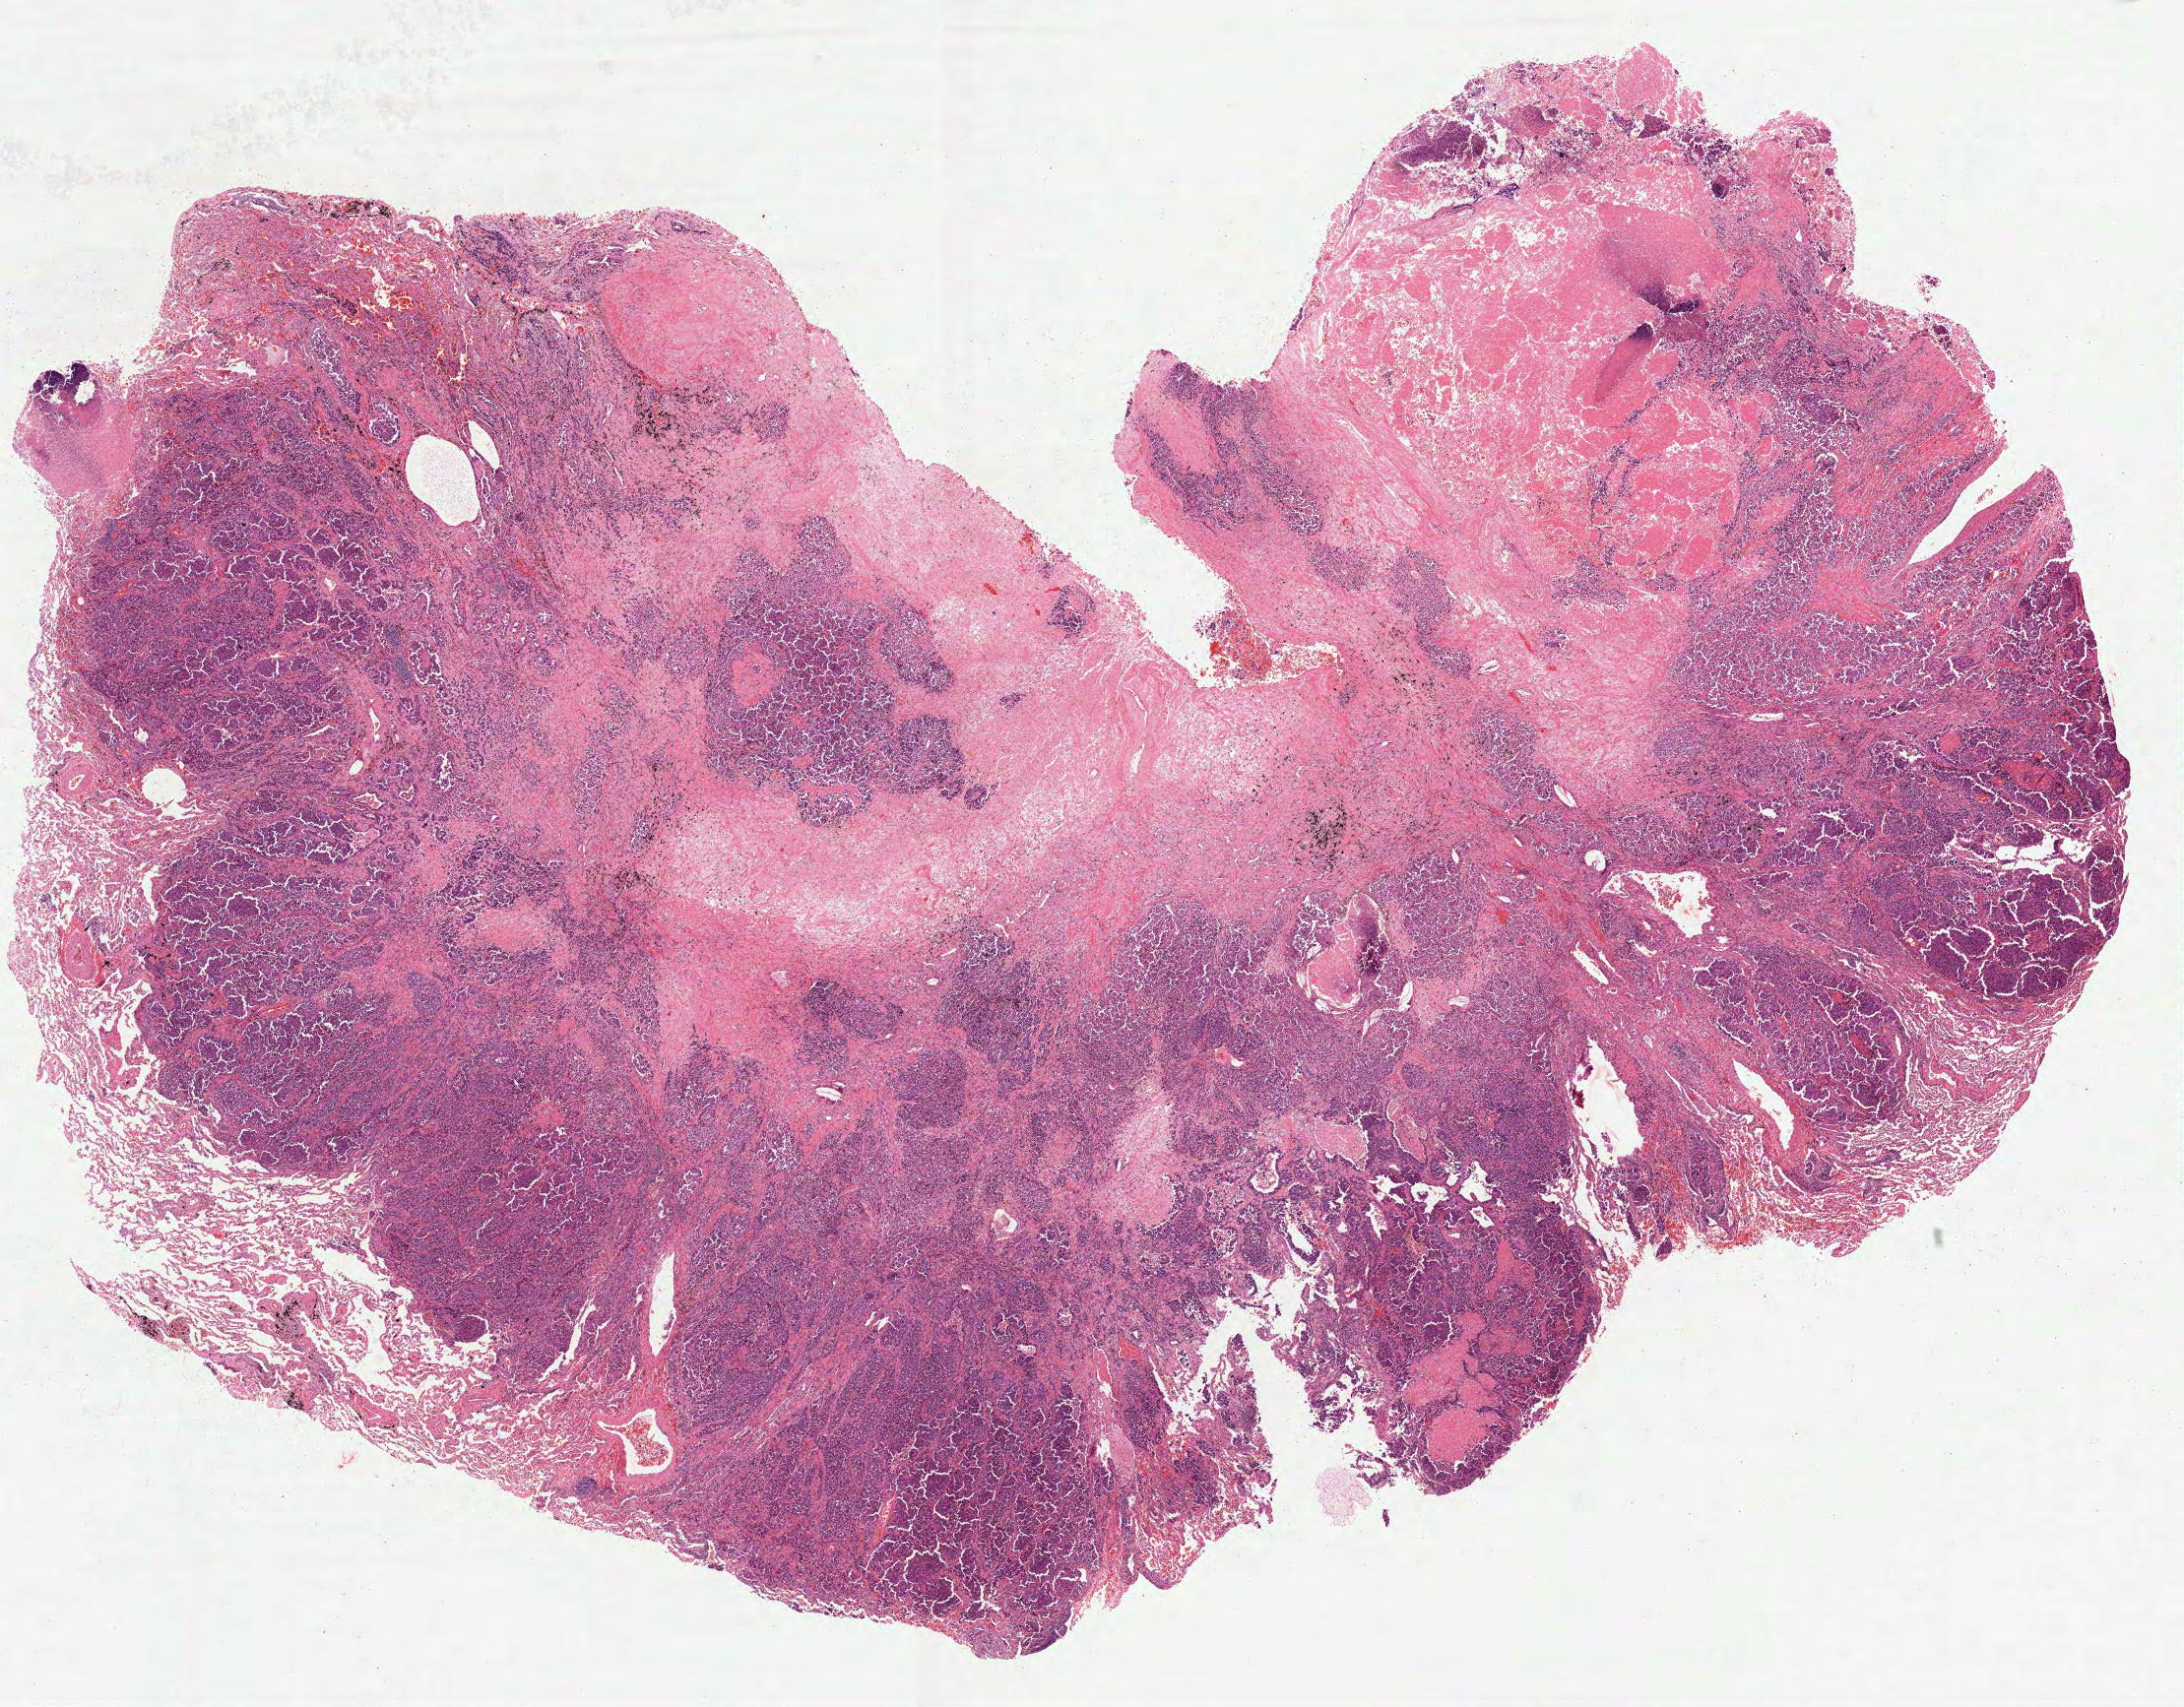
H&E-stained whole-slide image, a low-resolution overview of the entire scanned area, about 17.9 x 14.0 mm; FFPE section; lung, primary tumour sample. Male patient; age at initial diagnosis 44 years.
Histologic diagnosis: Adenocarcinoma, NOS (upper lobe, lung). AJCC pathologic stage: IB.